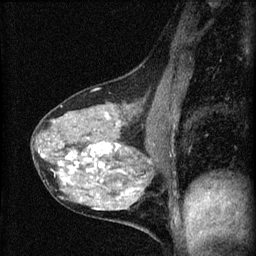
Breast MRI (dynamic contrast-enhanced), one sagittal slice; slice 29 of 60 in the series (ordered by position); dynamic contrast-enhanced series, image 2 of 4 at this slice position (ordered by acquisition); 1.5 T; TE 4.2 ms, TR 8.2 ms; 2 mm slice thickness; 256 × 256 image matrix, field of view 180 × 180 mm. Female patient, age 41 years.
Annotated regions visible in this slice (semi-automatically segmented with operator editing):
- analysis volume of interest (the breast-tissue region the enhancement analysis was run in; not a lesion): bounding box [x1, y1, x2, y2] px = [32, 91, 166, 210]
- tumour enhancement mask (voxels above the 70 % enhancement threshold inside the analysis volume of interest): [38, 123, 150, 210]